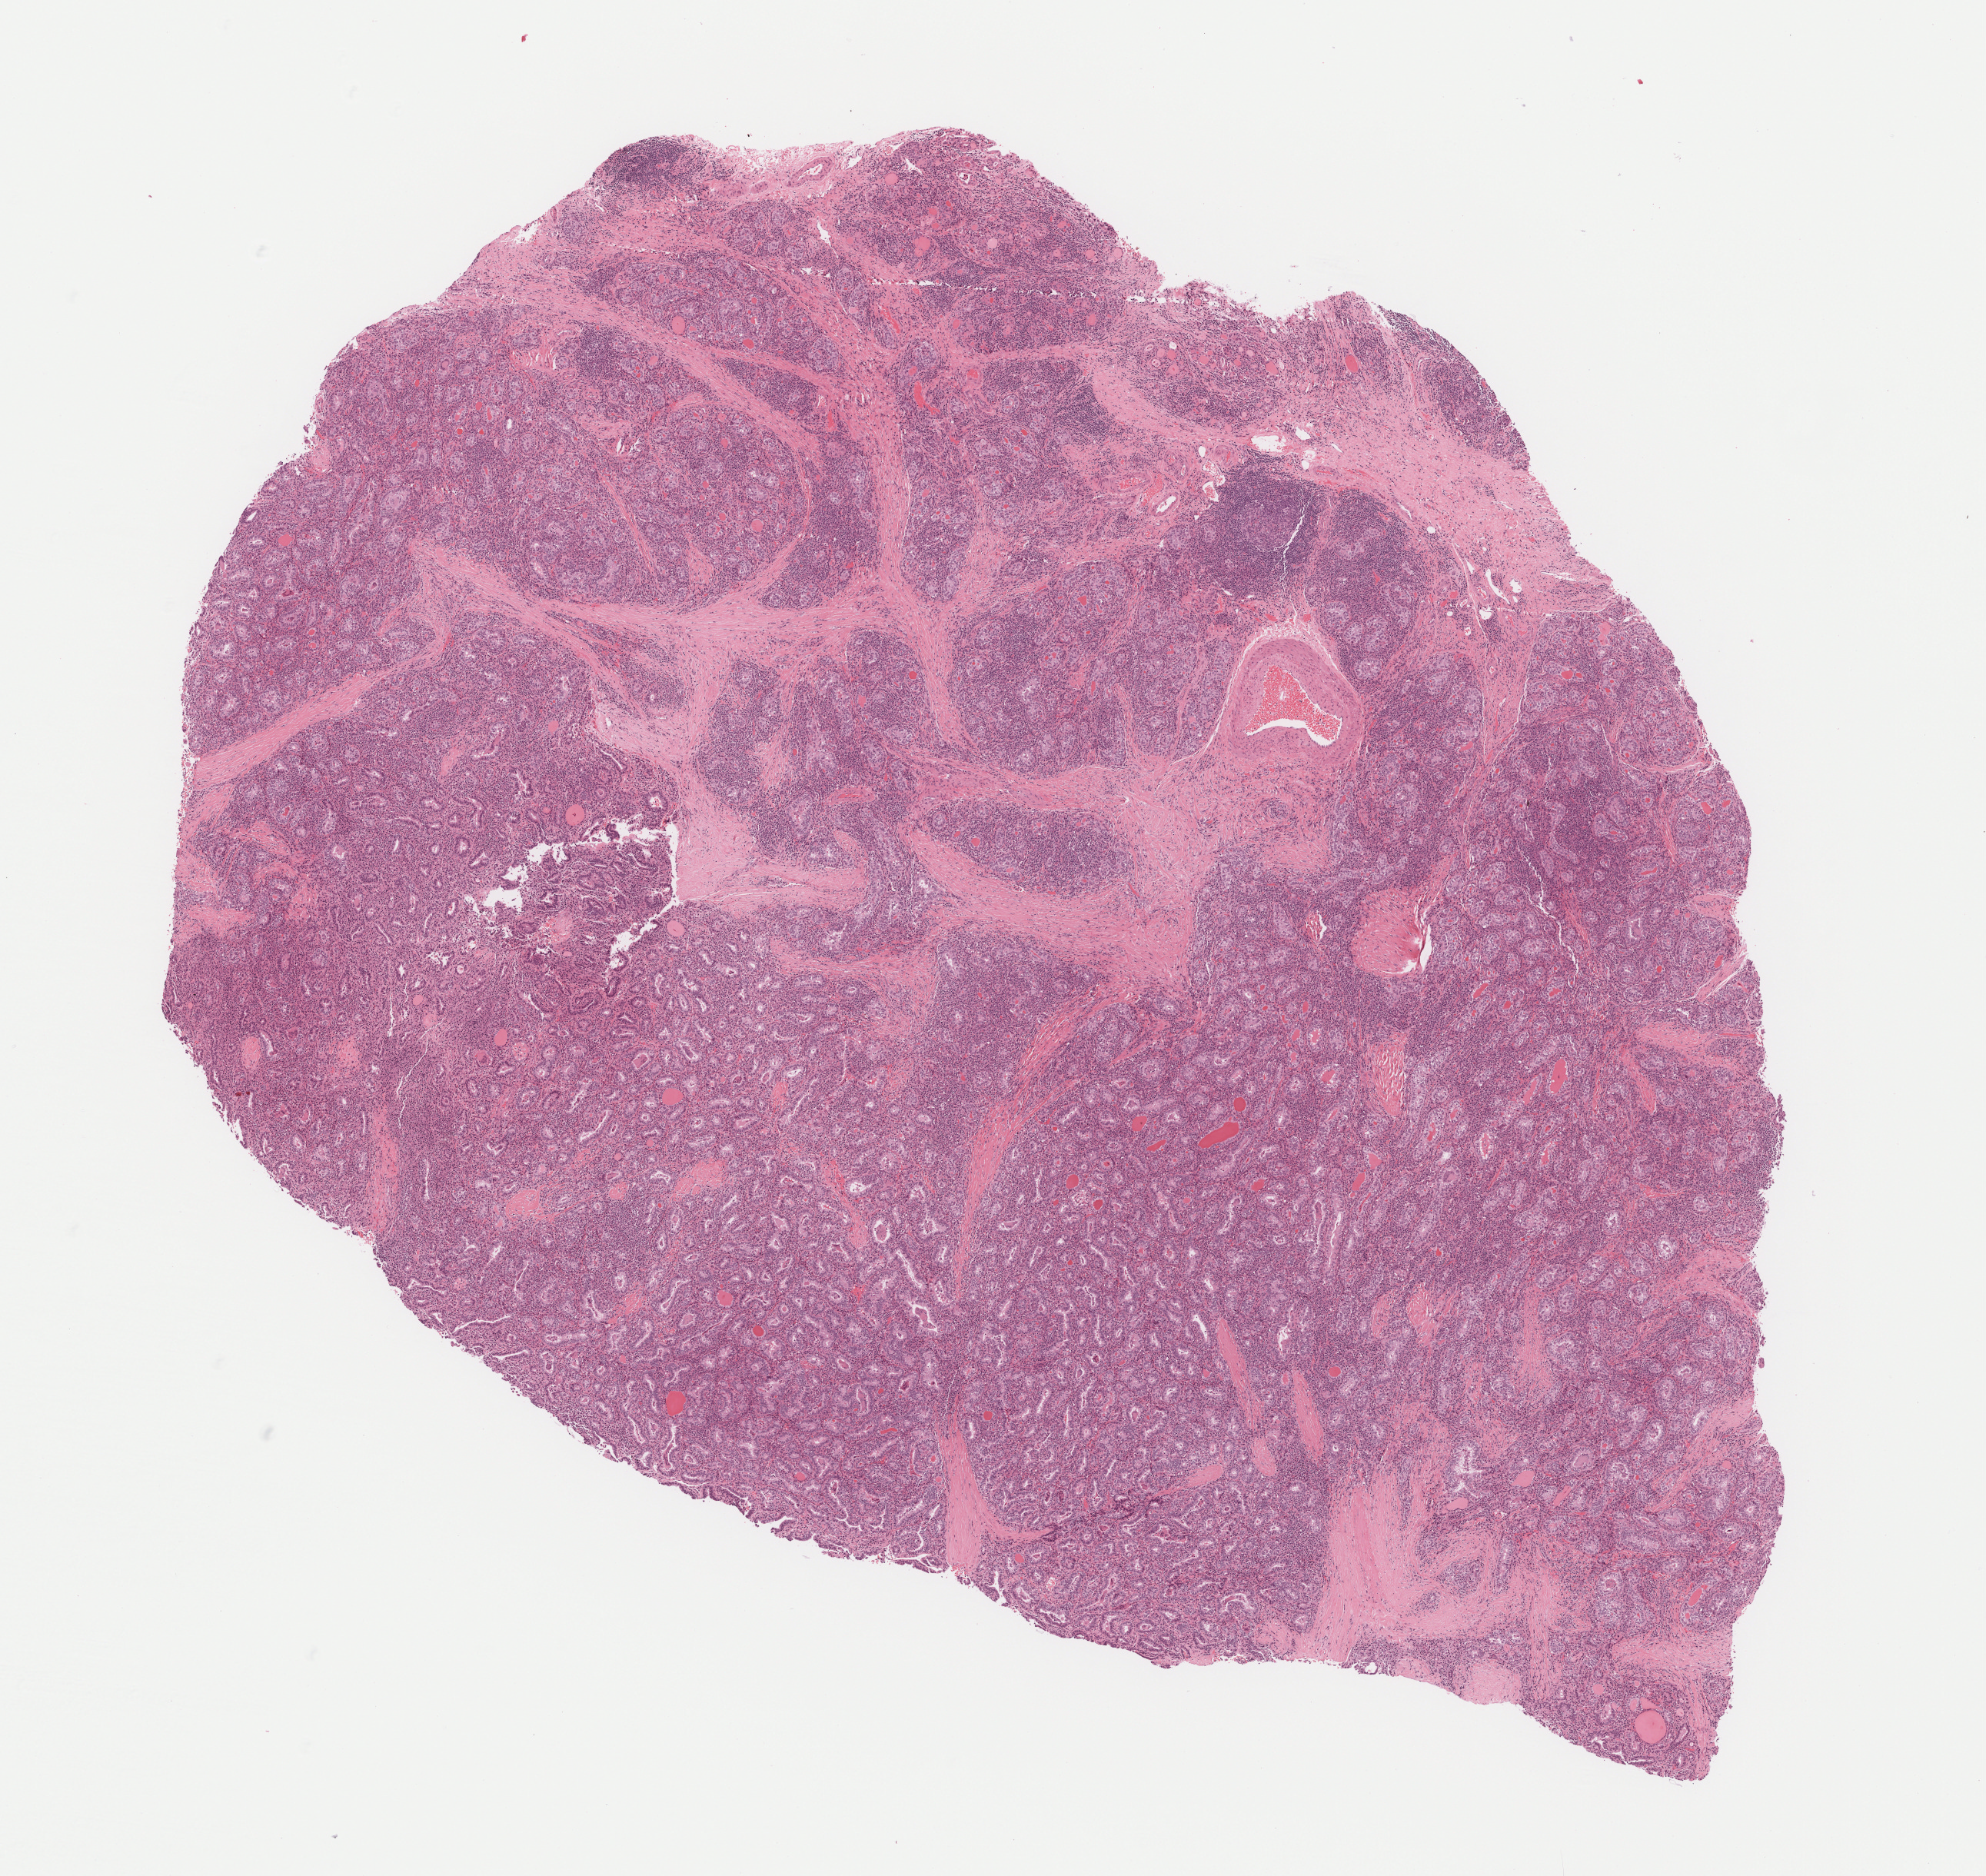
Whole-slide histology image, Hematoxylin and eosin (H&E) stained — whole scanned area (about 10.4 x 9.8 mm, acquisition: 40x scan) shown as a low-resolution overview. Formalin-fixed paraffin-embedded (FFPE) diagnostic section. Sample: primary tumour, thyroid. Patient: male, age at initial diagnosis 52 years.
Laterality: right. Diagnosis: Papillary adenocarcinoma, NOS. Lymph nodes positive (case pathology): 0 of 3 examined. AJCC pathologic stage: I (7th edition).